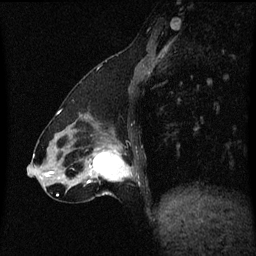
Breast MRI (dynamic contrast-enhanced), one sagittal slice. Position 19 of 60 along the scan axis. Dynamic contrast-enhanced series, image 2 of 3 at this slice position (ordered by acquisition). 1.5 T. TE 4.2 ms, TR 8.4 ms. 2 mm slice thickness. 256 × 256 image matrix, field of view 200 × 200 mm. Patient: female, 47 years.
Annotated regions visible in this slice (semi-automatic segmentation, software-assisted and operator-edited):
- analysis volume of interest (the breast-tissue region the enhancement analysis was run in; not a lesion): box from (x=81, y=140) to (x=135, y=197) px
- tumour enhancement mask (voxels above the 70 % enhancement threshold inside the analysis volume of interest): (x=87, y=146)–(x=132, y=183)